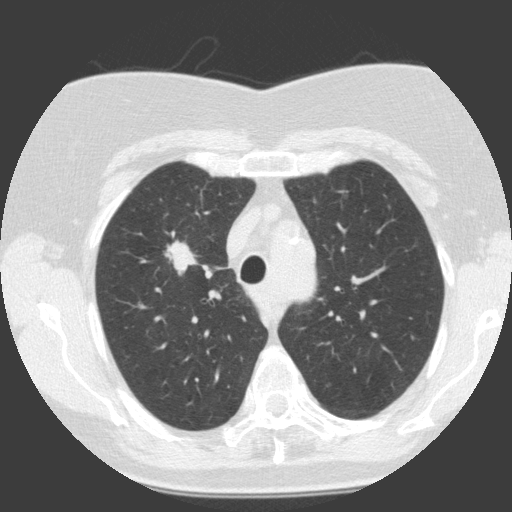
Low-dose screening chest CT, one axial slice; slice 107 of 146 in the series (ordered by position); 120 kVp; lung window (W 1500 / L -600 HU); 512 × 512 image matrix.
Structures marked on this image (expert manual segmentation):
- lesion 1 (tumor, upper lobe of right lung): bounding box (x1, y1, x2, y2) in pixels: (165, 240, 196, 276)